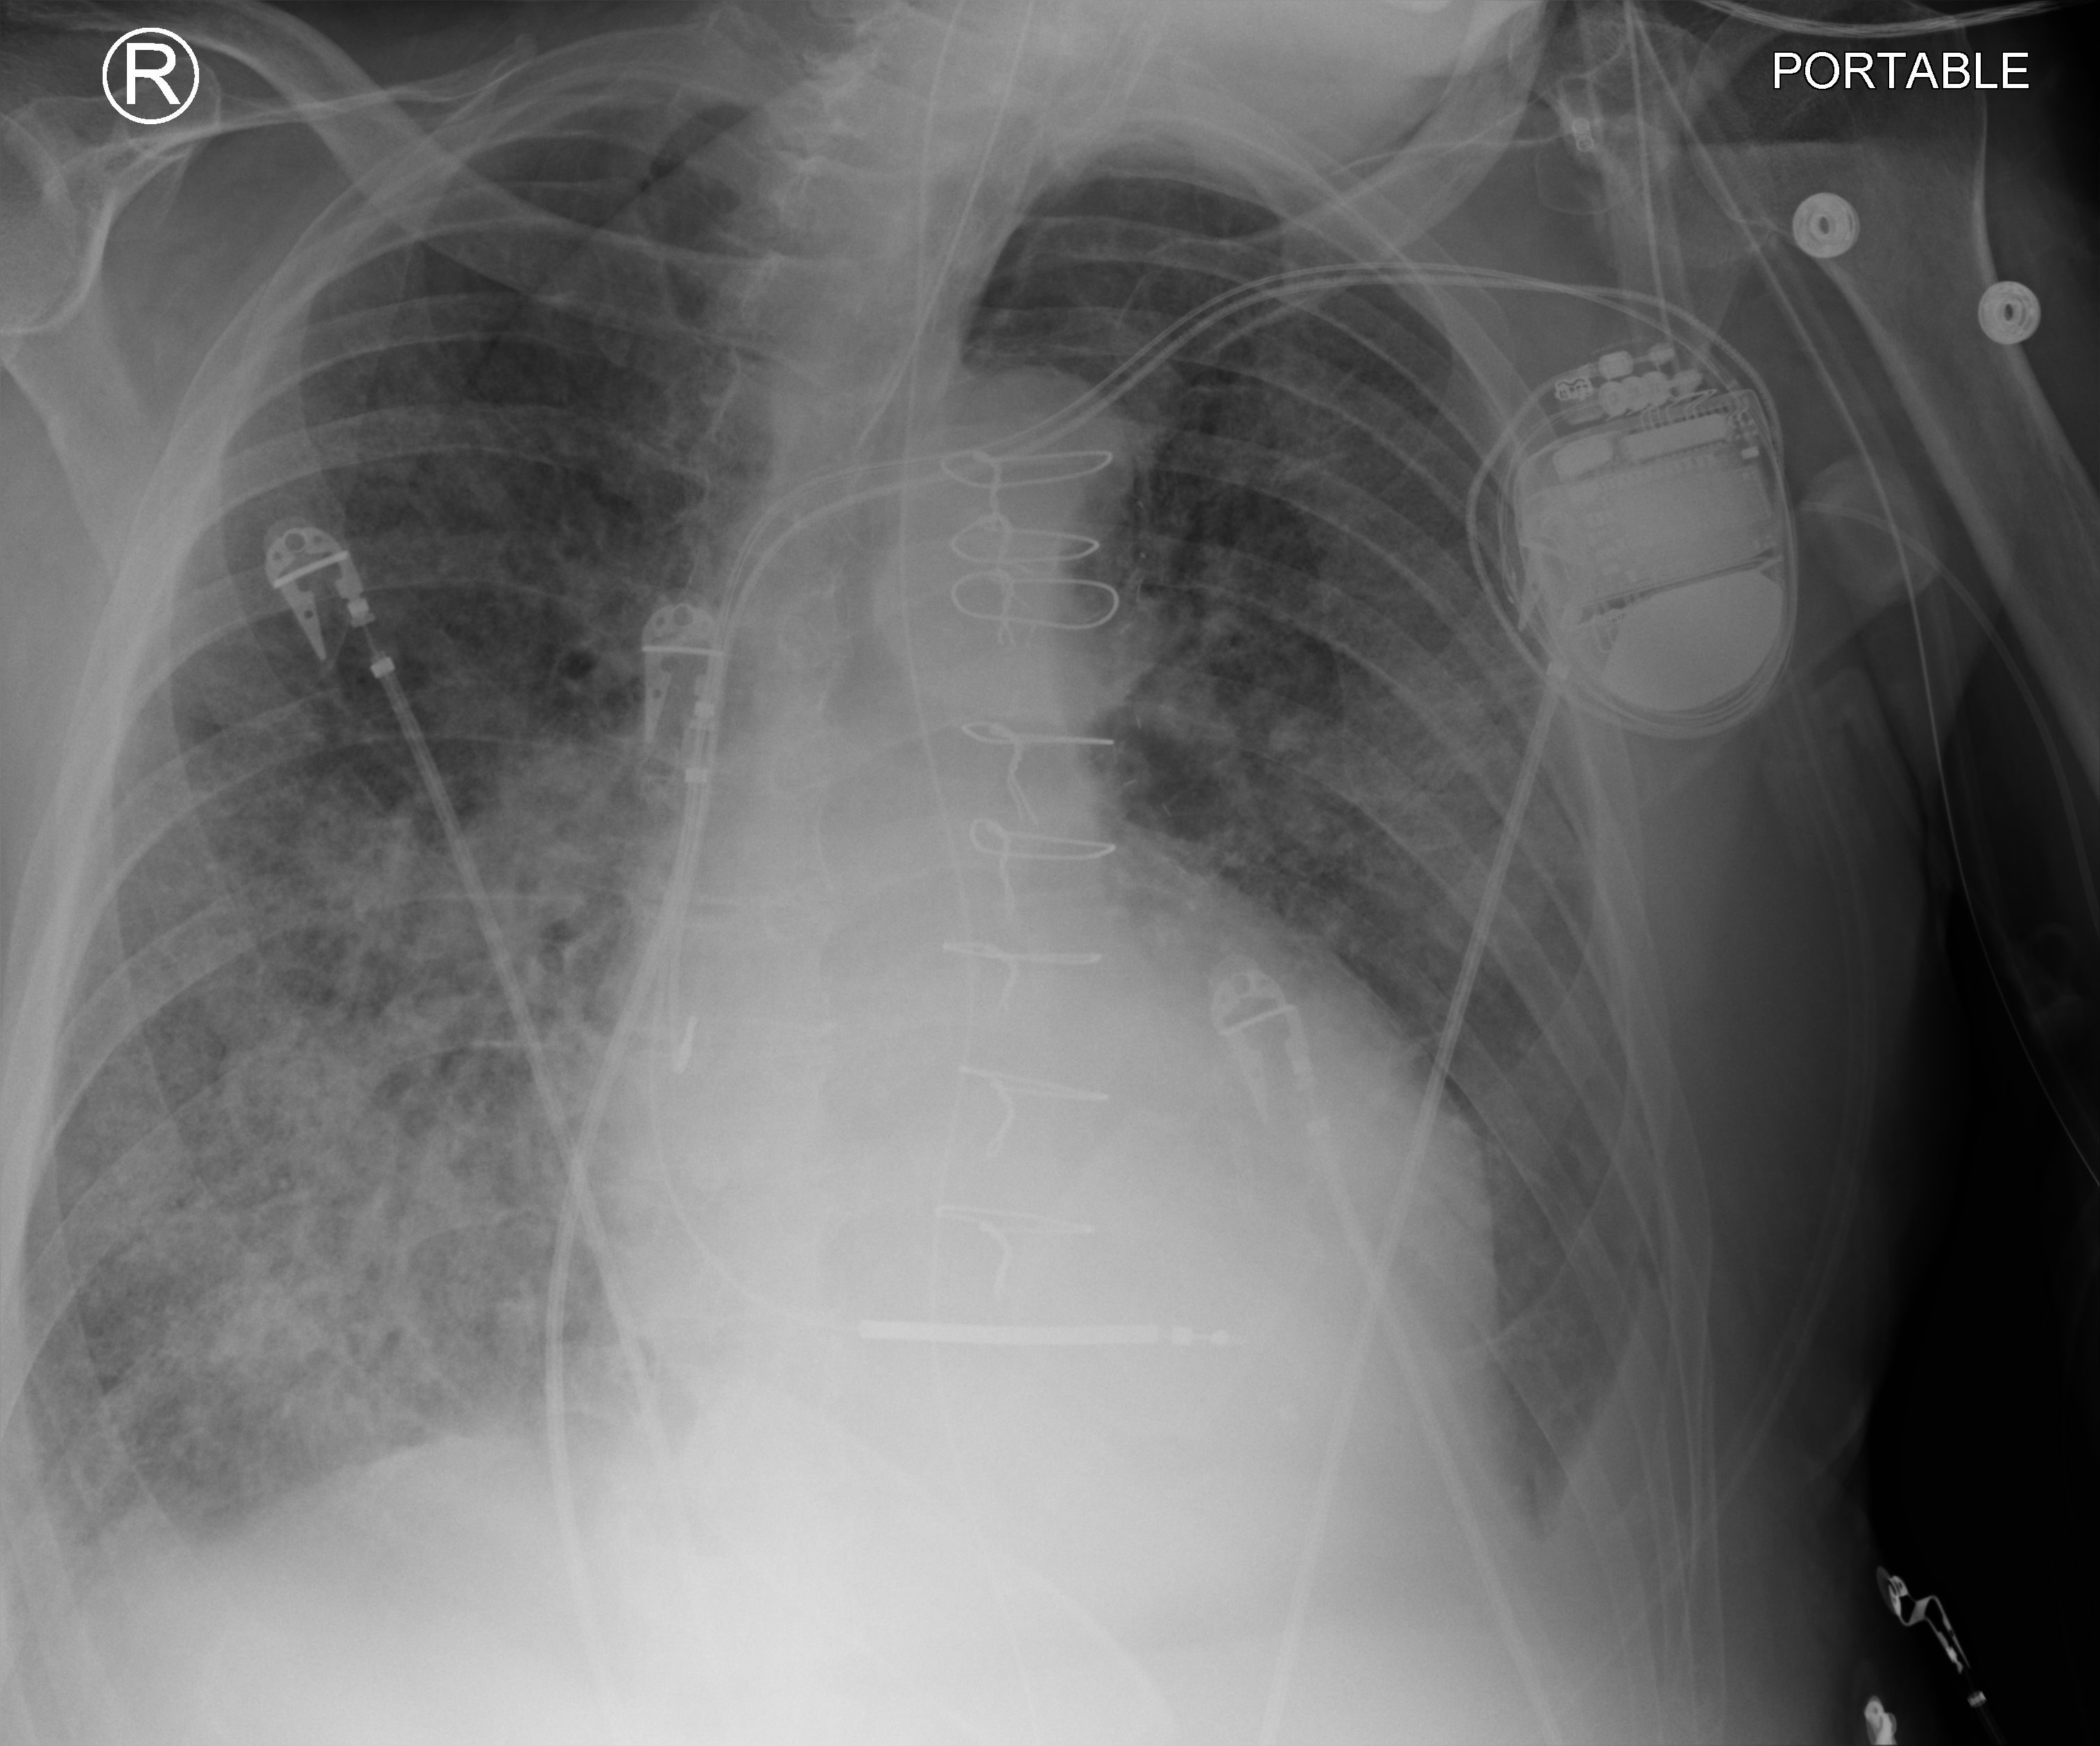
Bedside chest radiograph (computed radiography). Male patient hospitalised with COVID-19, age 75–90 years.
From the hospital-stay record, not from the radiograph (when in the stay this image was taken is not recorded):
- length of hospital stay: 11 days
- admitted to intensive care during this hospital stay: yes